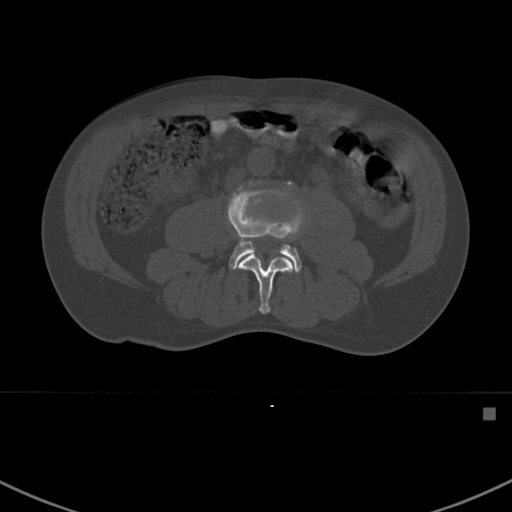
CT including the spine, one axial slice. Slice 253 of 412 in the series (ordered by position). Reconstruction kernel Br40s. Bone window (W 1800 / L 400 HU). 1.5 mm slice thickness. 512 × 512 image matrix, field of view 358 × 358 mm. Patient: male, 59 years. Case-level facts recorded for this patient, not image findings: primary cancer: prostate.
Outlined on this slice (semi-automatic segmentation, software-assisted and operator-edited):
- L3 vertebra: box from (x=236, y=252) to (x=295, y=314) px
- L4 vertebra: (x=227, y=182)–(x=304, y=272)